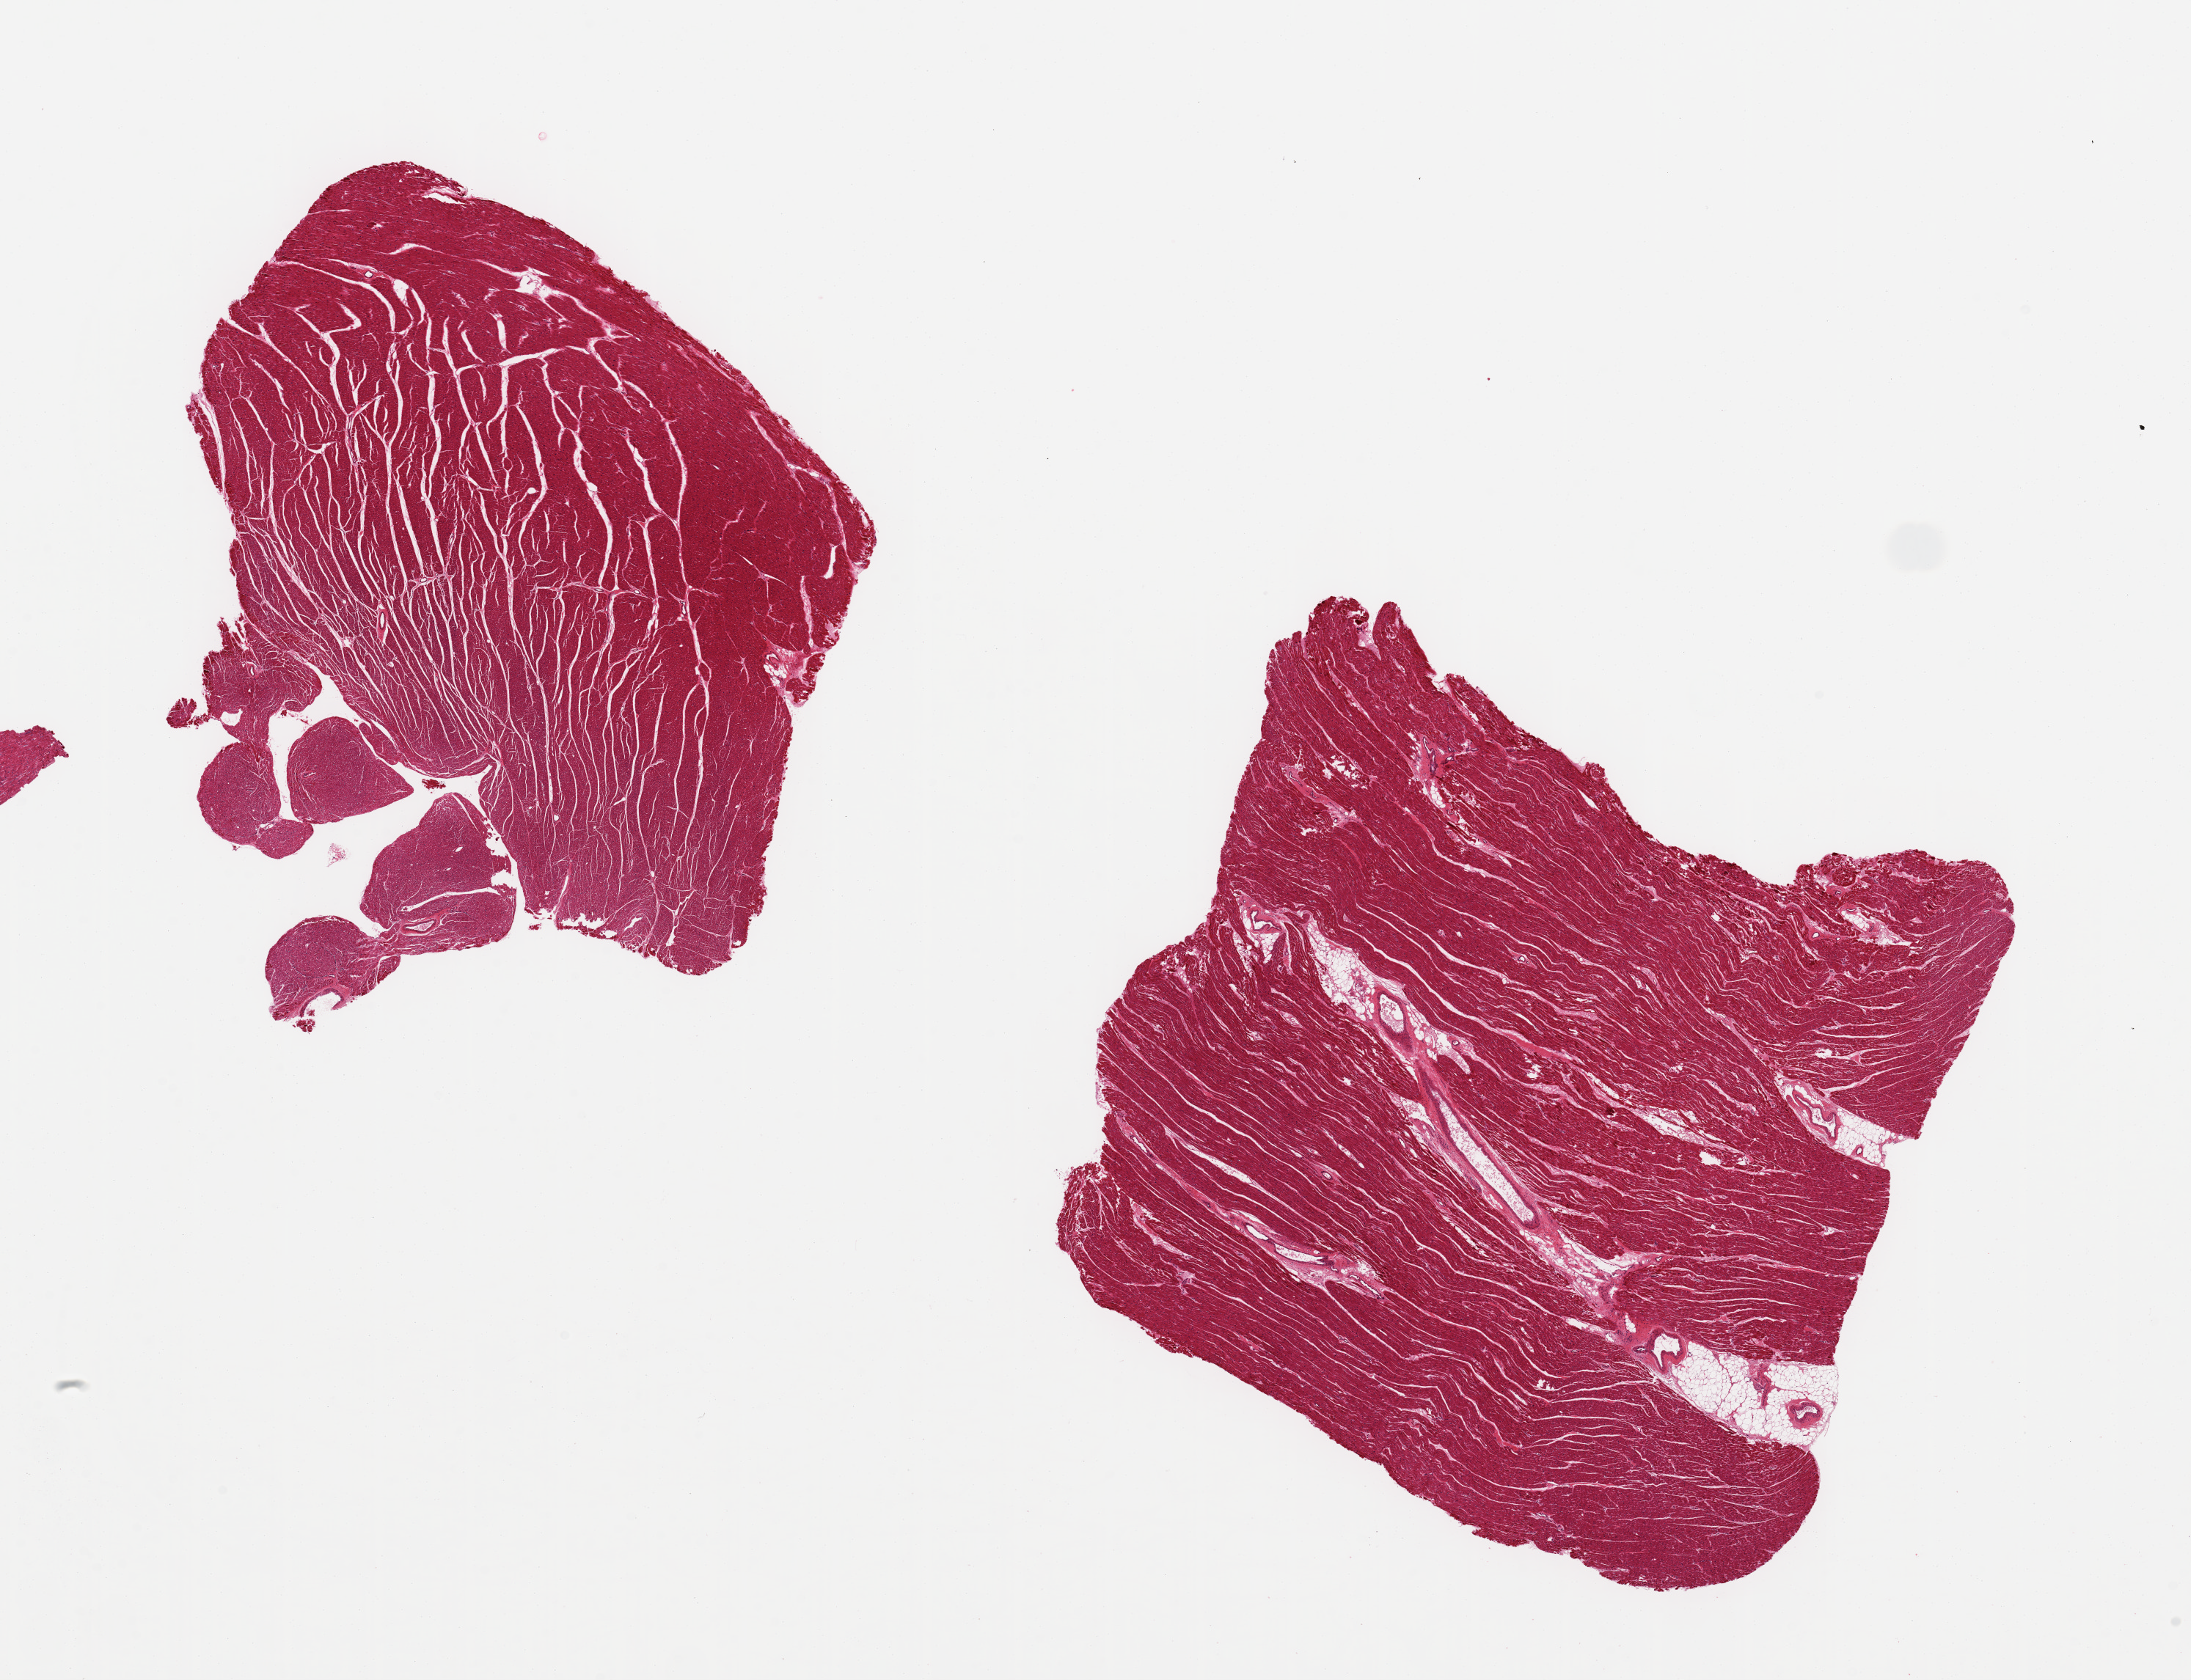
Whole-slide image, H&E stain — low-resolution overview of the scanned area, about 23.6 x 18.1 mm (slide scanned at 20x); PAXgene-fixed, paraffin-embedded tissue; target tissue: heart; tissue donor sample.
• reviewer comment on this tissue sample: 2 pieces, 7x5 & 7x8mm; includes papillary muscles